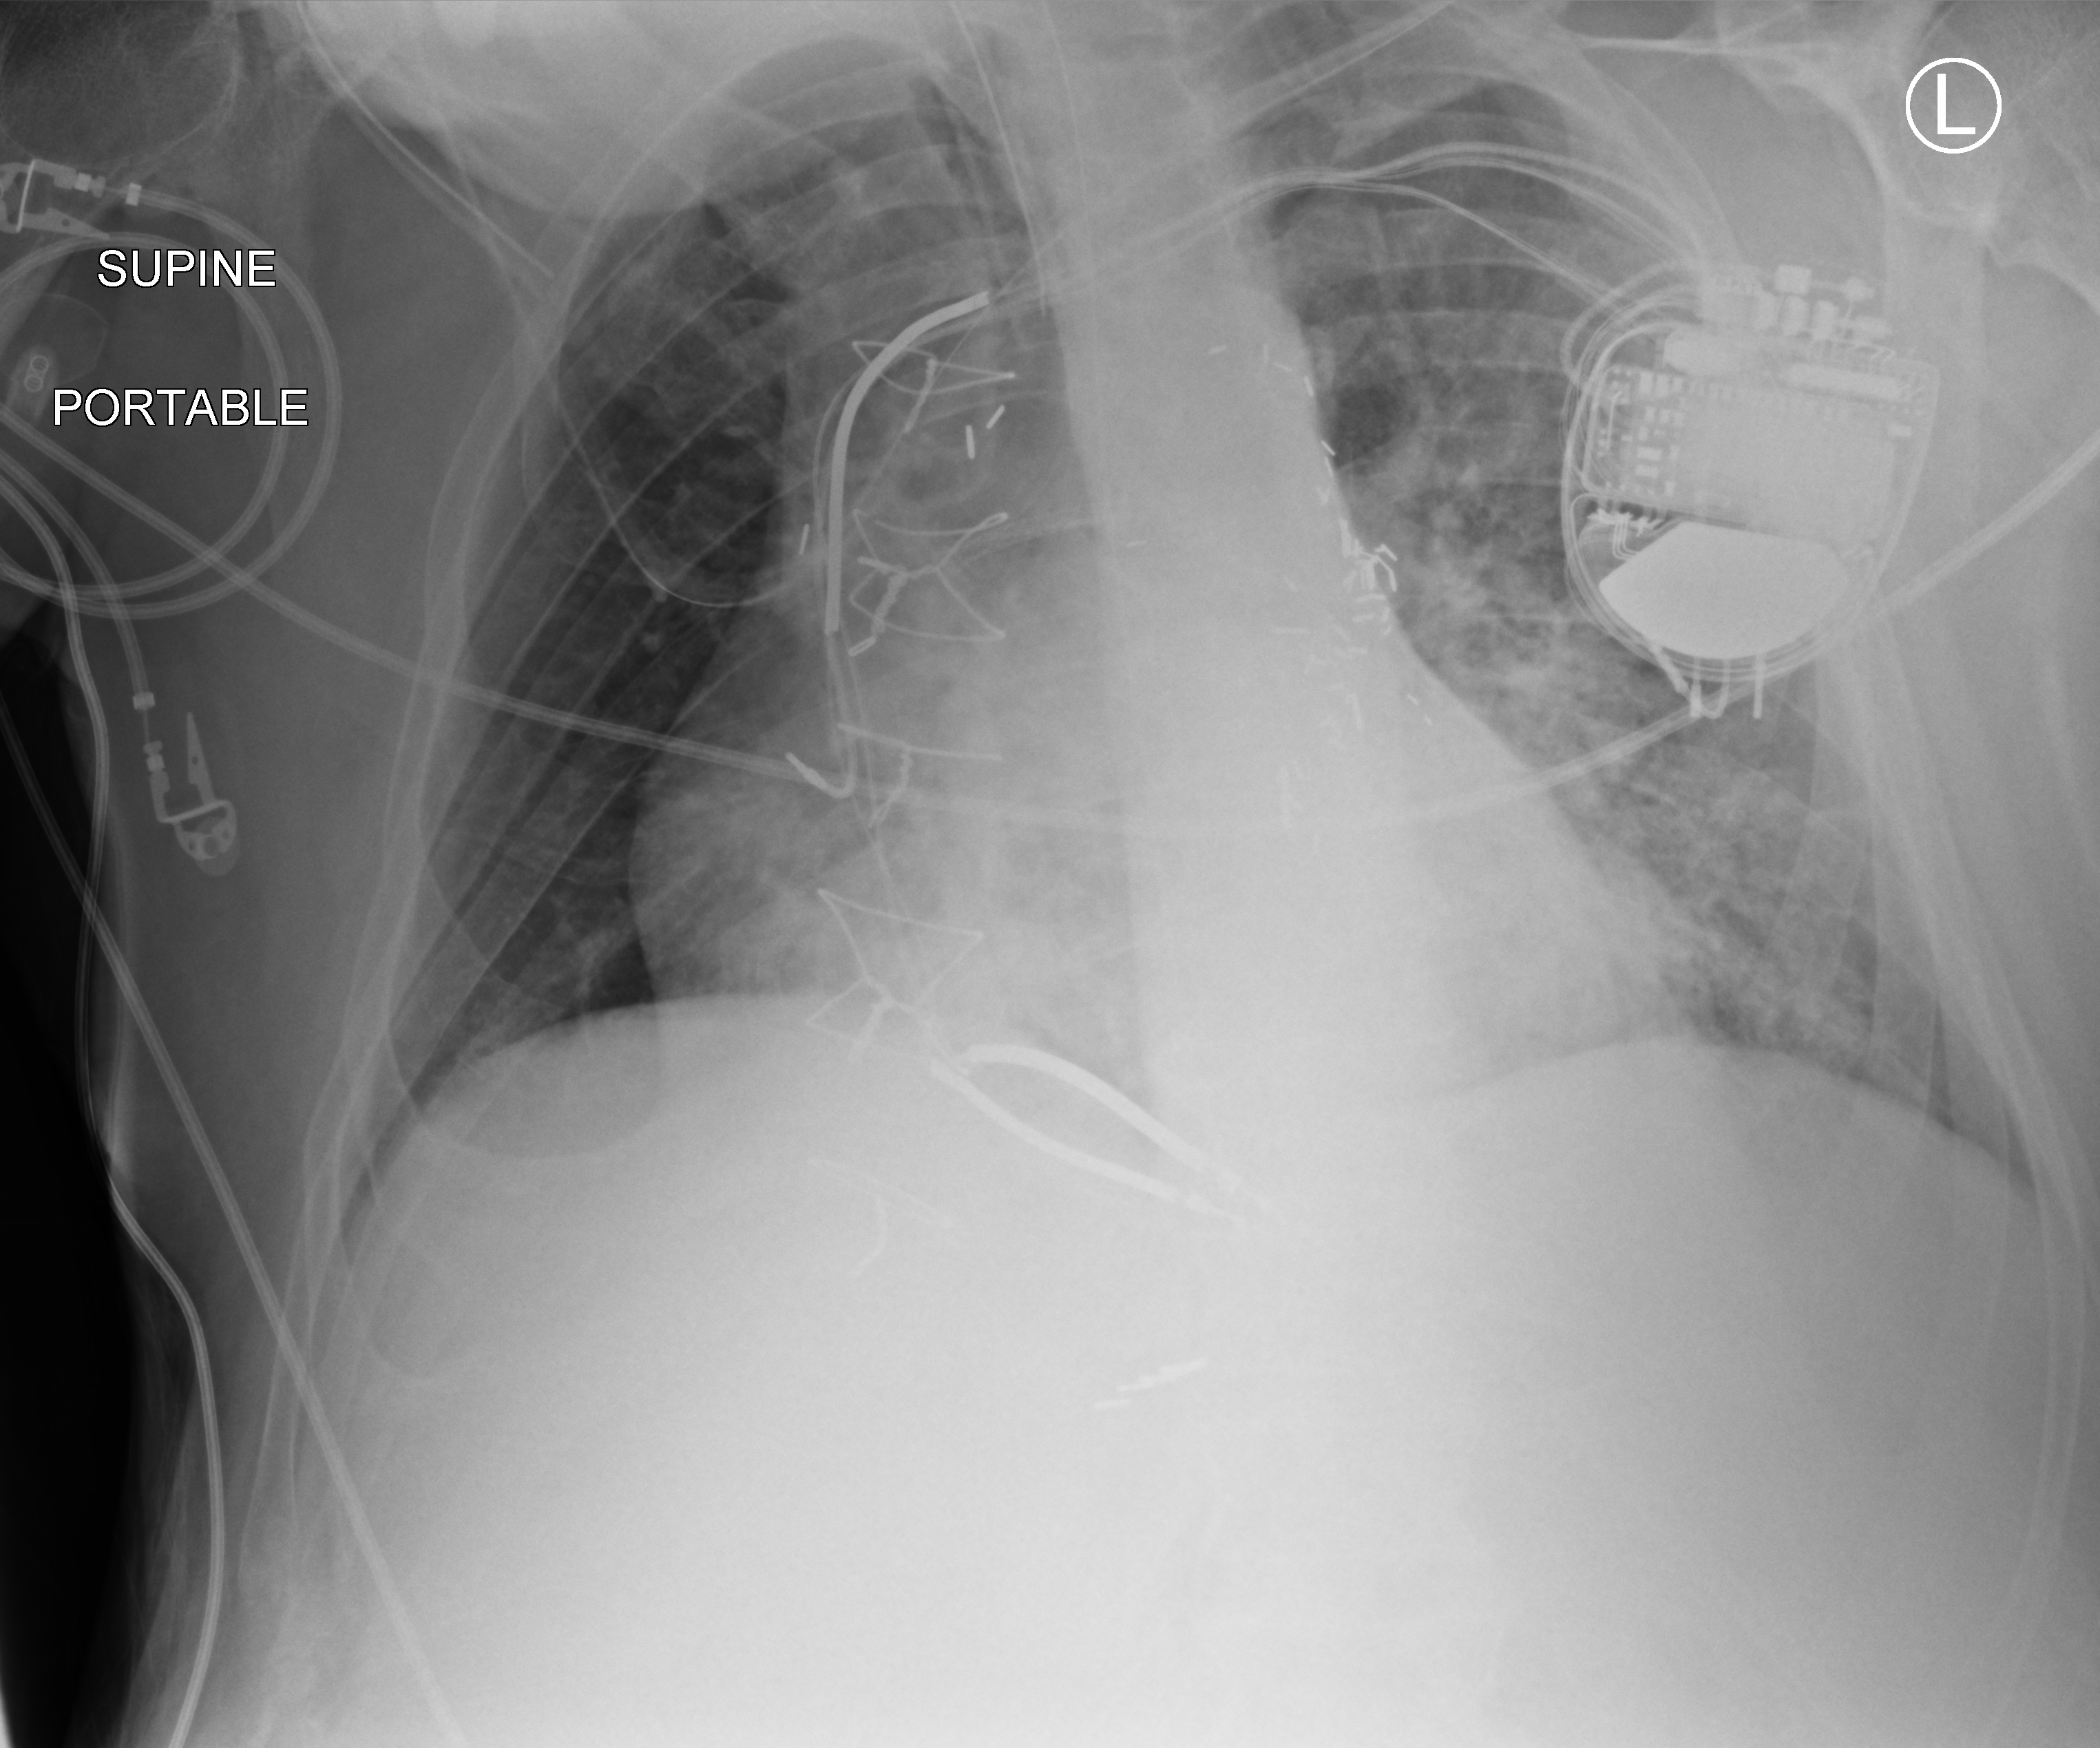
Portable chest radiograph; anteroposterior (AP) projection. Patient hospitalised with COVID-19; male, aged 60–74 years.
Hospital-stay facts (about this admission, not read from this image; timing relative to this image not recorded):
- diabetes (admission record): yes
- admitted to intensive care during this hospital stay: yes
- mechanically ventilated during this hospital stay: yes